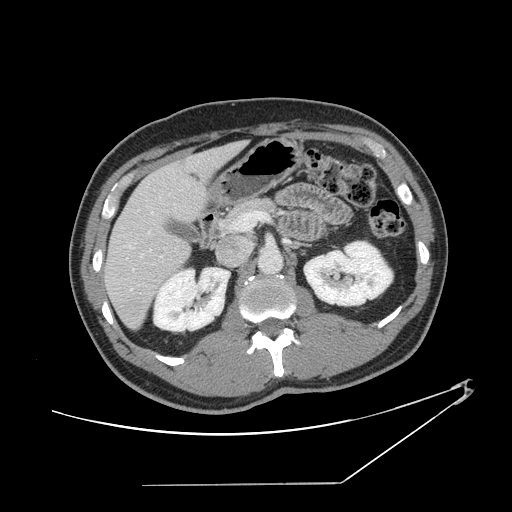
Contrast-enhanced abdominal CT, one axial slice. Slice 72 of 152 in the series (ordered by position). Reconstruction kernel STANDARD. 120 kVp. Soft-tissue window (W 400 / L 40 HU). 2.5 mm slice thickness. 512 × 512 image matrix. Male patient, age 45 years. Case-level facts recorded for this patient, not image findings: diagnosis: colorectal cancer liver metastases, imaged before liver resection; multiple liver metastases: no; largest metastasis: 1 cm; disease in both lobes: no.
Outlined on this slice (outlined manually by an expert reader):
- hepatic veins: bounding box (x1, y1, x2, y2) in pixels: (124, 197, 175, 290)
- liver: (106, 143, 243, 328)
- planned liver remnant (the part of the liver to remain after resection): (105, 160, 205, 329)
- portal vein (with intrahepatic branches): (233, 211, 268, 231)